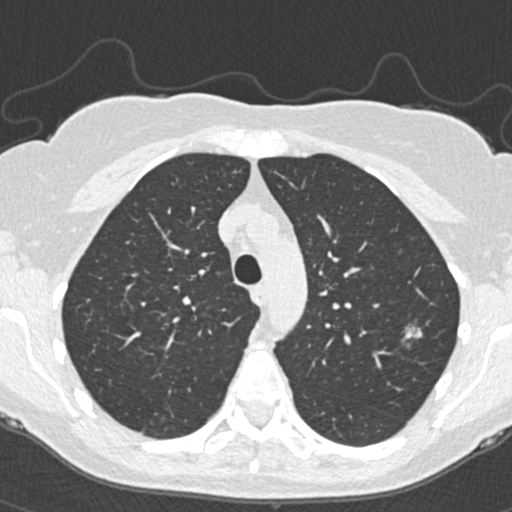
Low-dose screening chest CT, one axial slice; slice 267 of 350 in the series (ordered by position); 120 kVp; lung window (W 1500 / L -600 HU); 1 mm slice thickness; 512 × 512 image matrix, field of view 298 × 298 mm.
Annotated regions visible in this slice (outlined manually by an expert reader):
- lesion 1 (tumor, upper lobe of left lung): bounding box (x1, y1, x2, y2) in pixels: (404, 326, 423, 339)